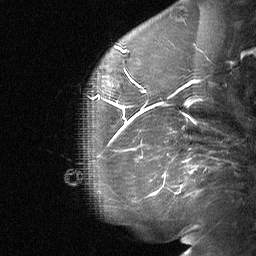
Breast MRI (dynamic contrast-enhanced), one sagittal slice. Dynamic contrast-enhanced study with each time point stored as its own series, time point 2 of 3 at this slice position (early post-contrast, ordered by acquisition time). 1.5 T. TE 4.8 ms, TR 27 ms. 2 mm slice thickness. 256 × 256 image matrix, field of view 200 × 200 mm. Patient: female, 60 years. Case-level facts recorded for this patient, not image findings: setting: breast cancer imaged before/during neoadjuvant chemotherapy; receptor status: HR-positive, HER2-negative.
Outlined on this slice (semi-automatic segmentation, software-assisted and operator-edited):
- analysis volume of interest (the breast-tissue region the enhancement analysis was run in; not a lesion): bounding box (x1, y1, x2, y2) in pixels: (91, 56, 139, 104)
- tumour enhancement mask (voxels above the 90 % enhancement threshold inside the analysis volume of interest): (97, 82, 139, 104)